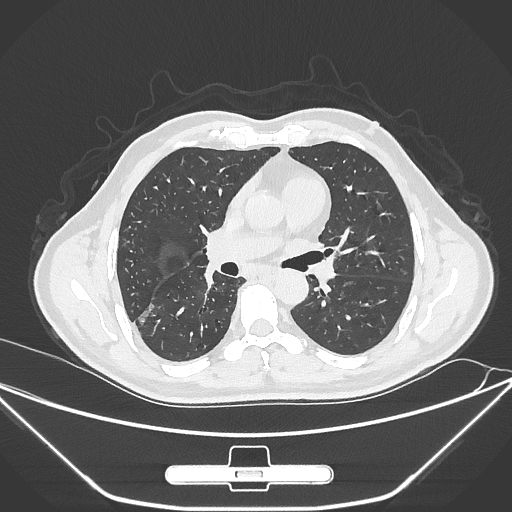
Chest CT, one axial slice. Position 159 of 310 along the scan axis. Lung window (W 1500 / L -600 HU). 1 mm slice thickness. 512 × 512 image matrix, field of view 398 × 398 mm. Patient: male, 71 years. Case-level facts recorded for this patient, not image findings: clinical TNM (as recorded): T1c N0 M0; histopathological grade: G2.
Outlined on this slice (bounding box drawn by a radiologist):
- lung tumour (recorded histology: adenocarcinoma): bounding box (x1, y1, x2, y2) in pixels: (125, 290, 161, 344)